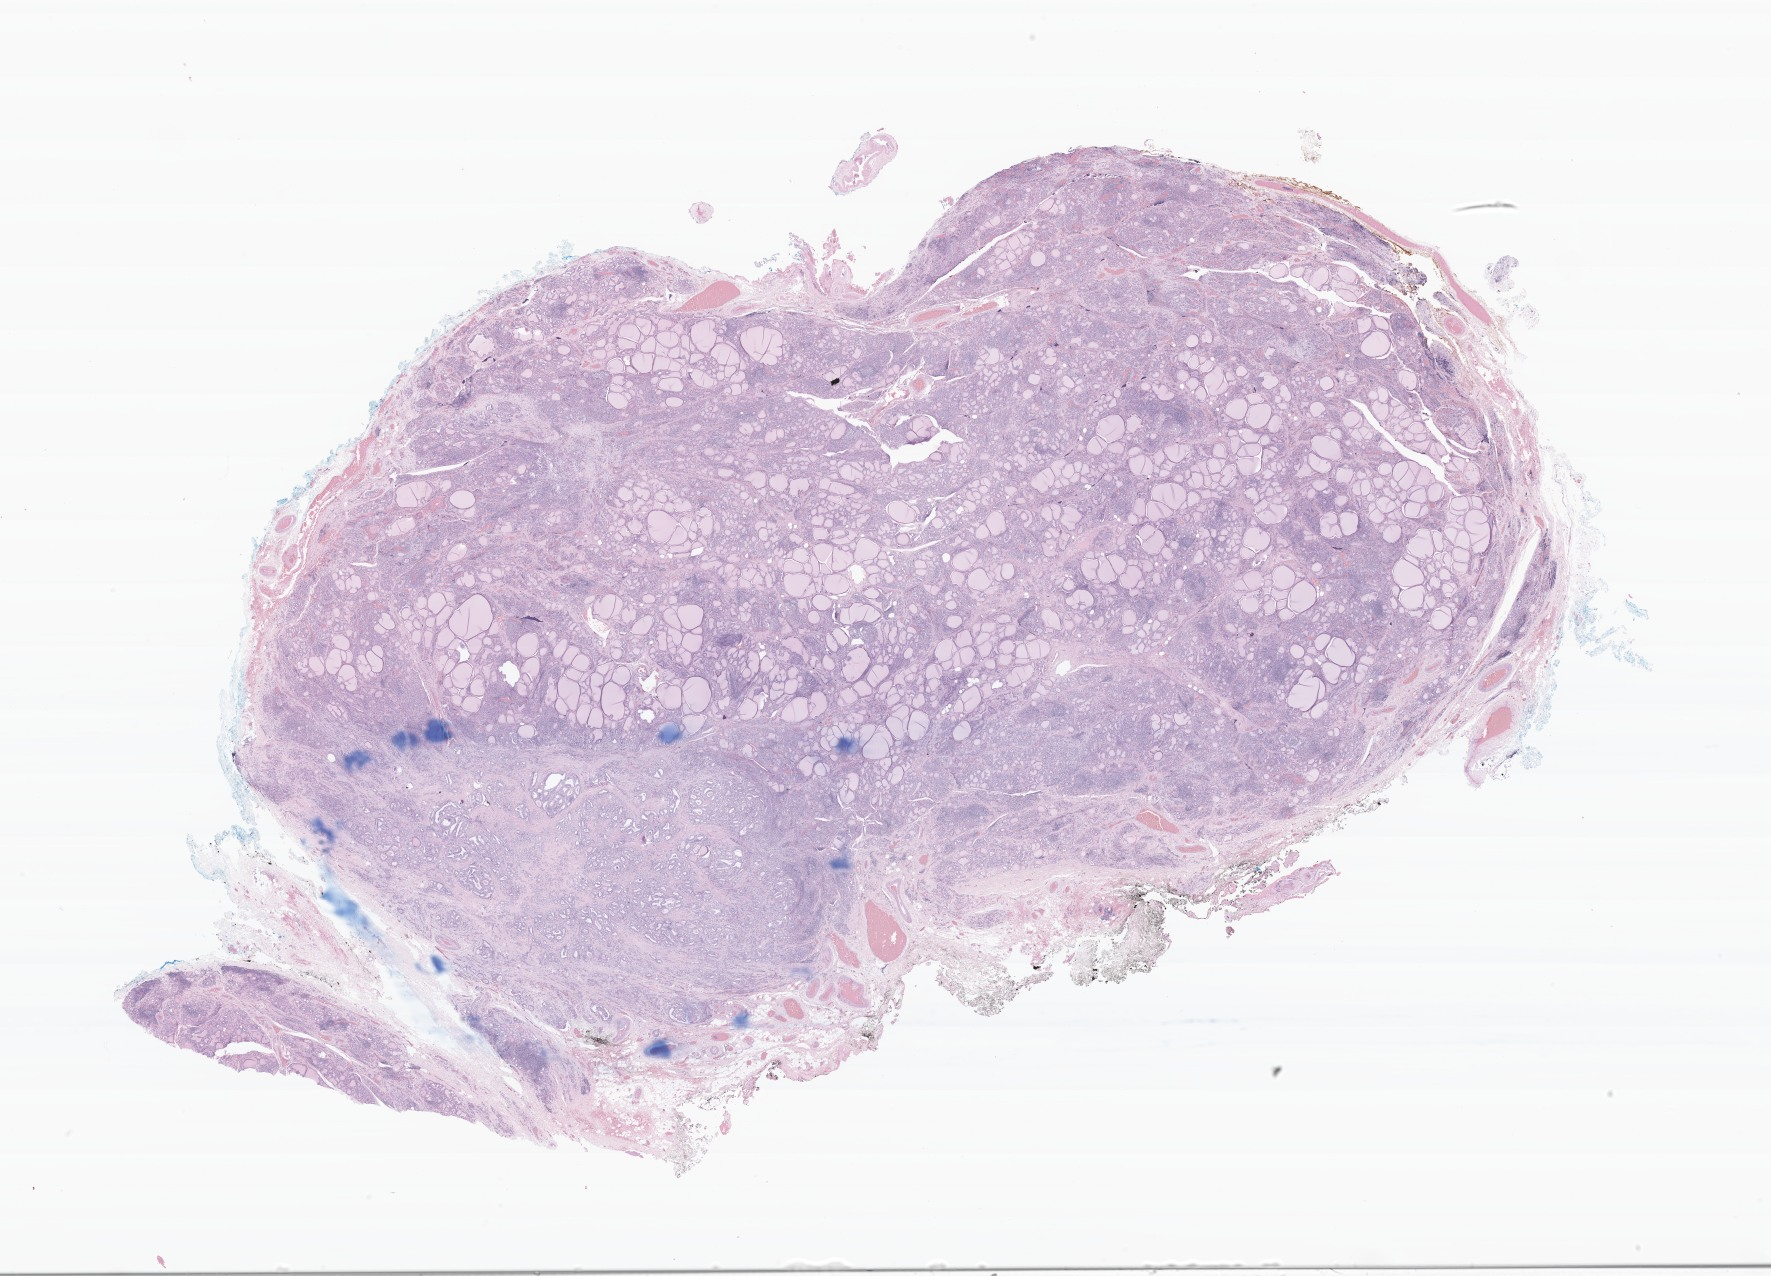
Haematoxylin and eosin whole-slide image of tumor tissue from the thyroid, whole scanned area (about 29.8 x 21.5 mm) shown as a low-resolution overview. Formalin-fixed paraffin-embedded section. Patient: female, age 192 months (16 years).
Diagnosis (ICD-O-3 morphology term): Papillary carcinoma, NOS.